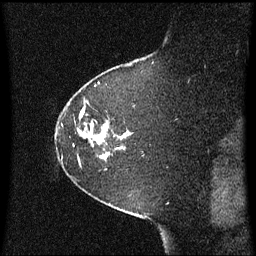
Breast MRI (dynamic contrast-enhanced), one sagittal slice; slice 52 of 60 in the series (ordered by position); dynamic contrast-enhanced series, image 2 of 3 at this slice position (ordered by acquisition); 1.5 T; TE 4.2 ms, TR 8.4 ms; 256 × 256 image matrix, field of view 210 × 210 mm. Patient: female, 60 years. Case-level facts recorded for this patient, not image findings: setting: breast cancer imaged before/during neoadjuvant chemotherapy; receptor status: triple-negative.
Annotated regions visible in this slice (semi-automatically segmented with operator editing):
- analysis volume of interest (the breast-tissue region the enhancement analysis was run in; not a lesion): bounding box (x1, y1, x2, y2) in pixels: (57, 100, 132, 164)
- tumour enhancement mask (voxels above the 70 % enhancement threshold inside the analysis volume of interest): (83, 130, 108, 158)